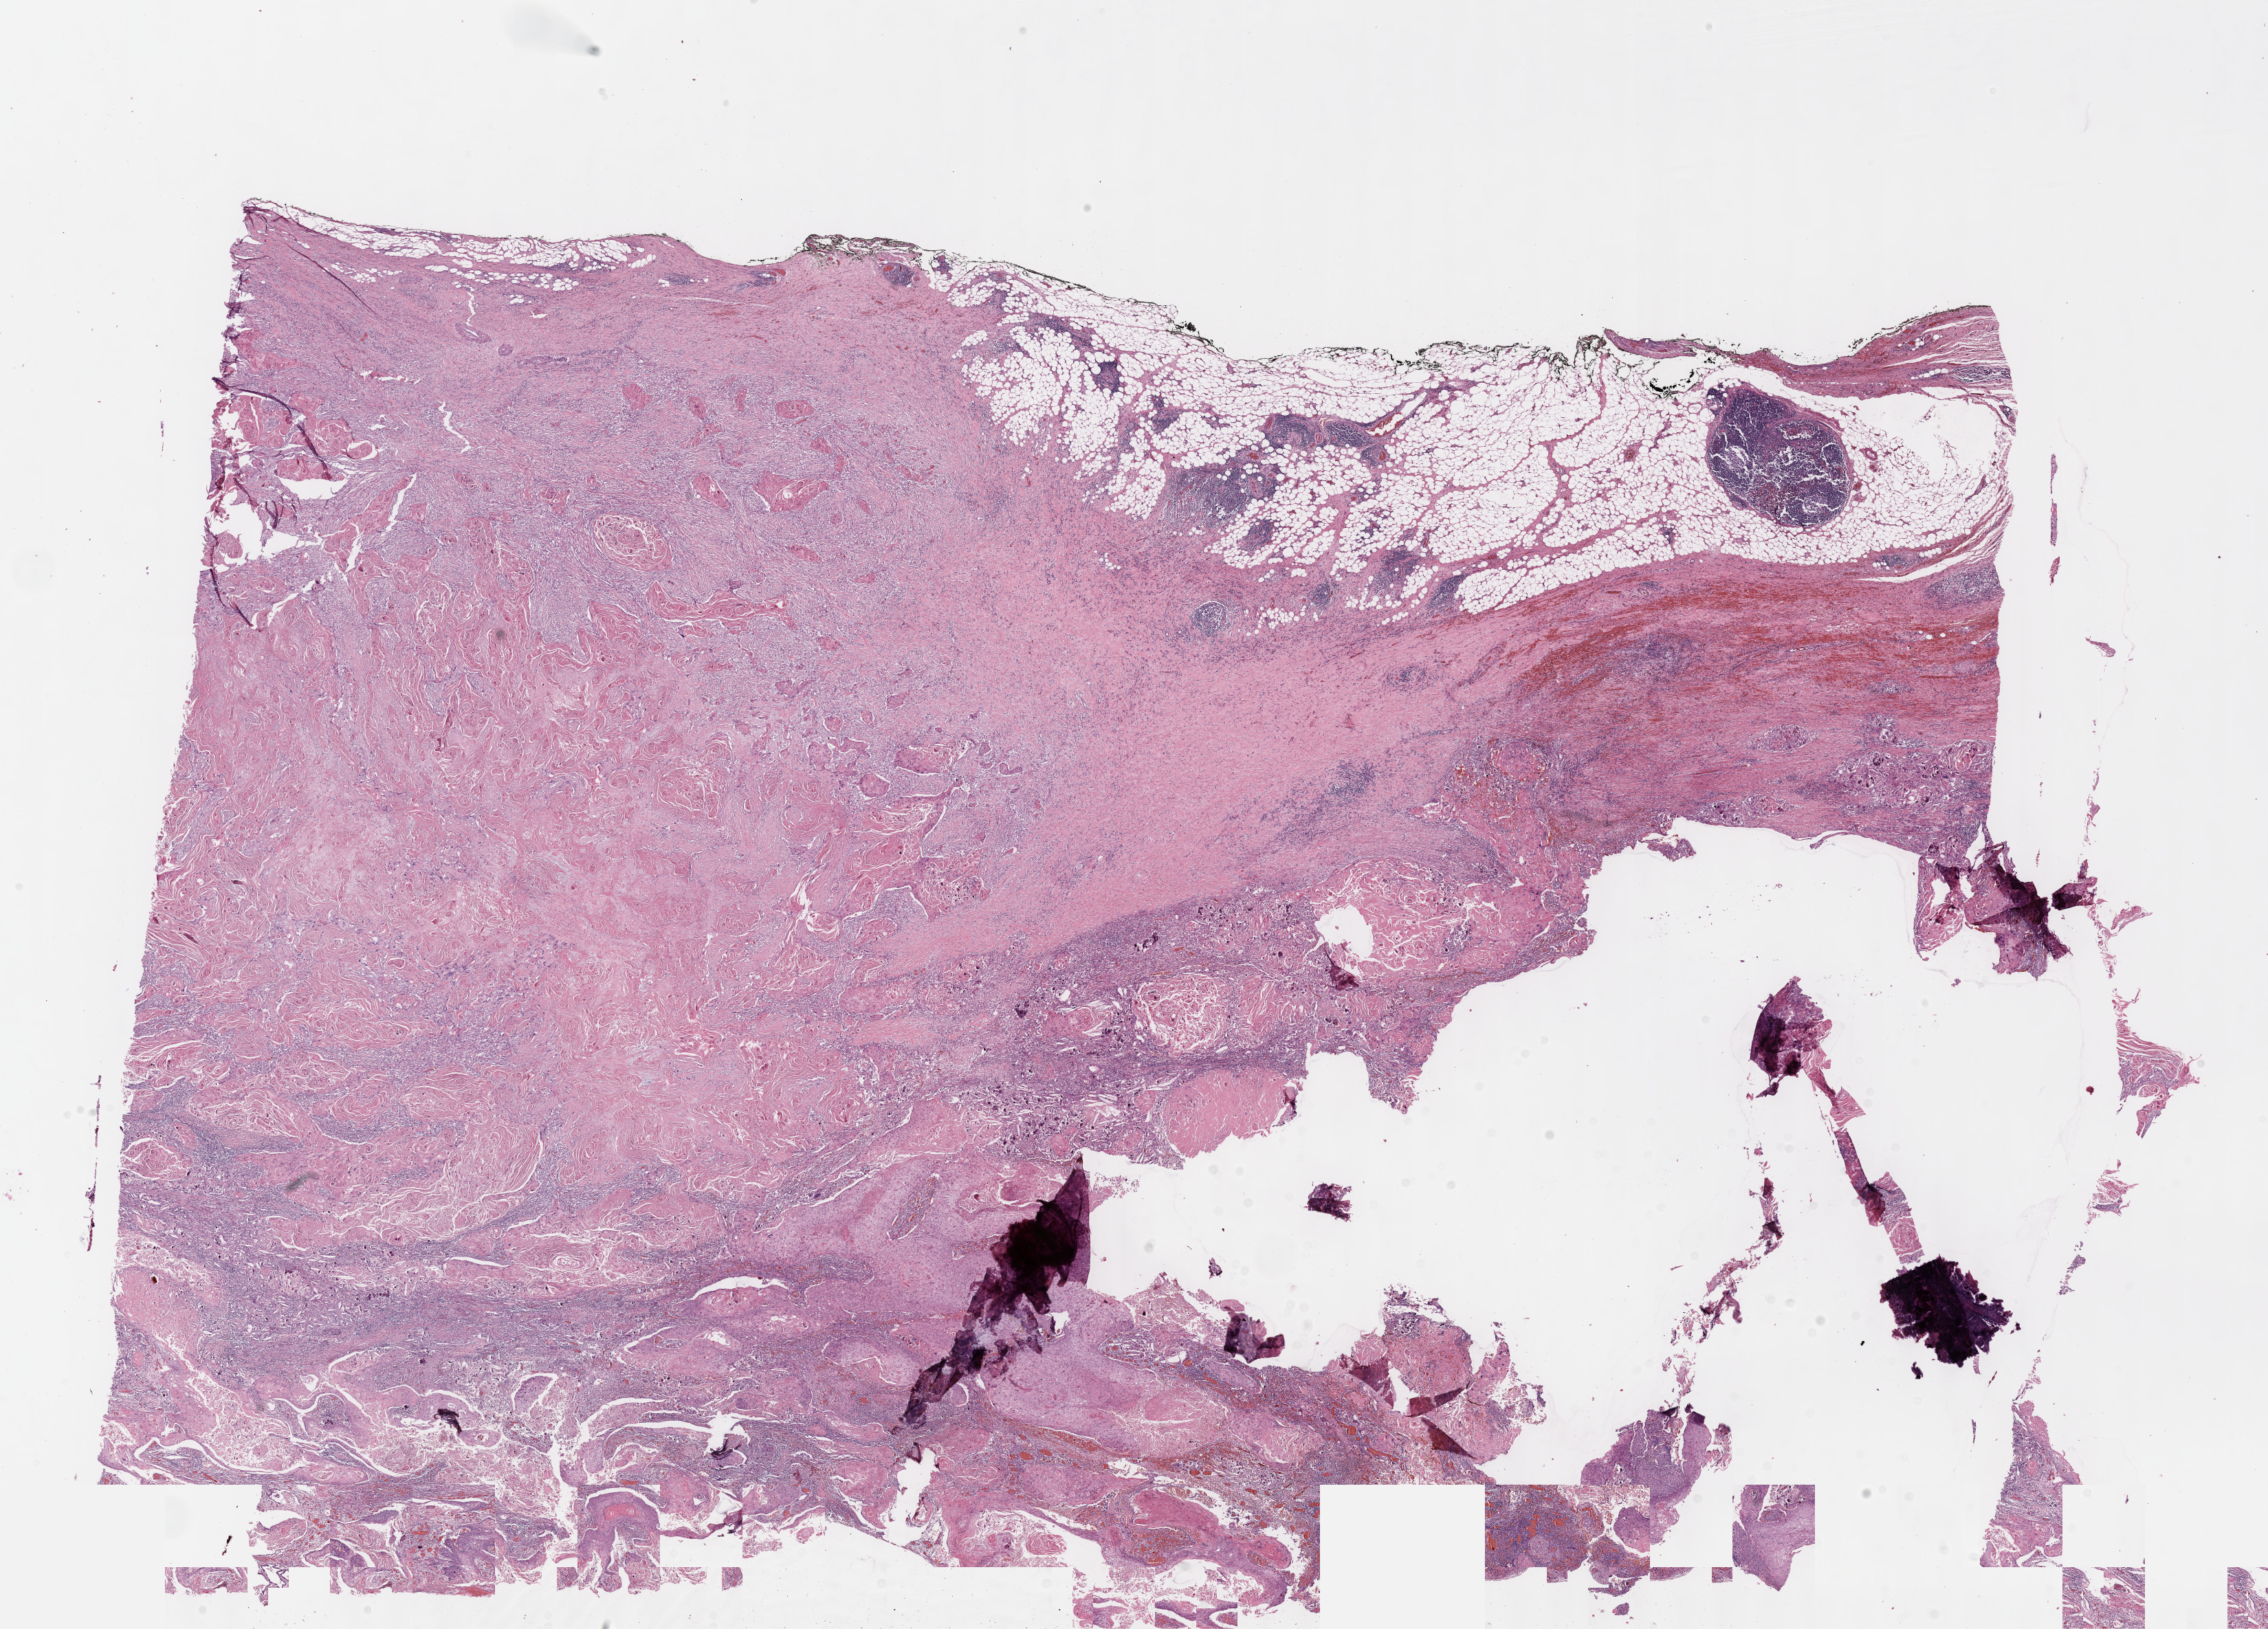
Digitized H&E tissue section (whole slide), shown as a low-resolution overview of the whole scanned area (about 26.7 x 19.2 mm, slide scanned at 40x). Formalin-fixed paraffin-embedded (FFPE) diagnostic section. Esophagus, primary tumour sample. Male patient; age at initial diagnosis 64 years. Histologic grade: G2 (moderately differentiated).
Lymph nodes positive (case pathology): 0 of 17 examined. AJCC pathologic stage: IIA (7th edition). Diagnosis: Squamous cell carcinoma, NOS (lower third of esophagus).